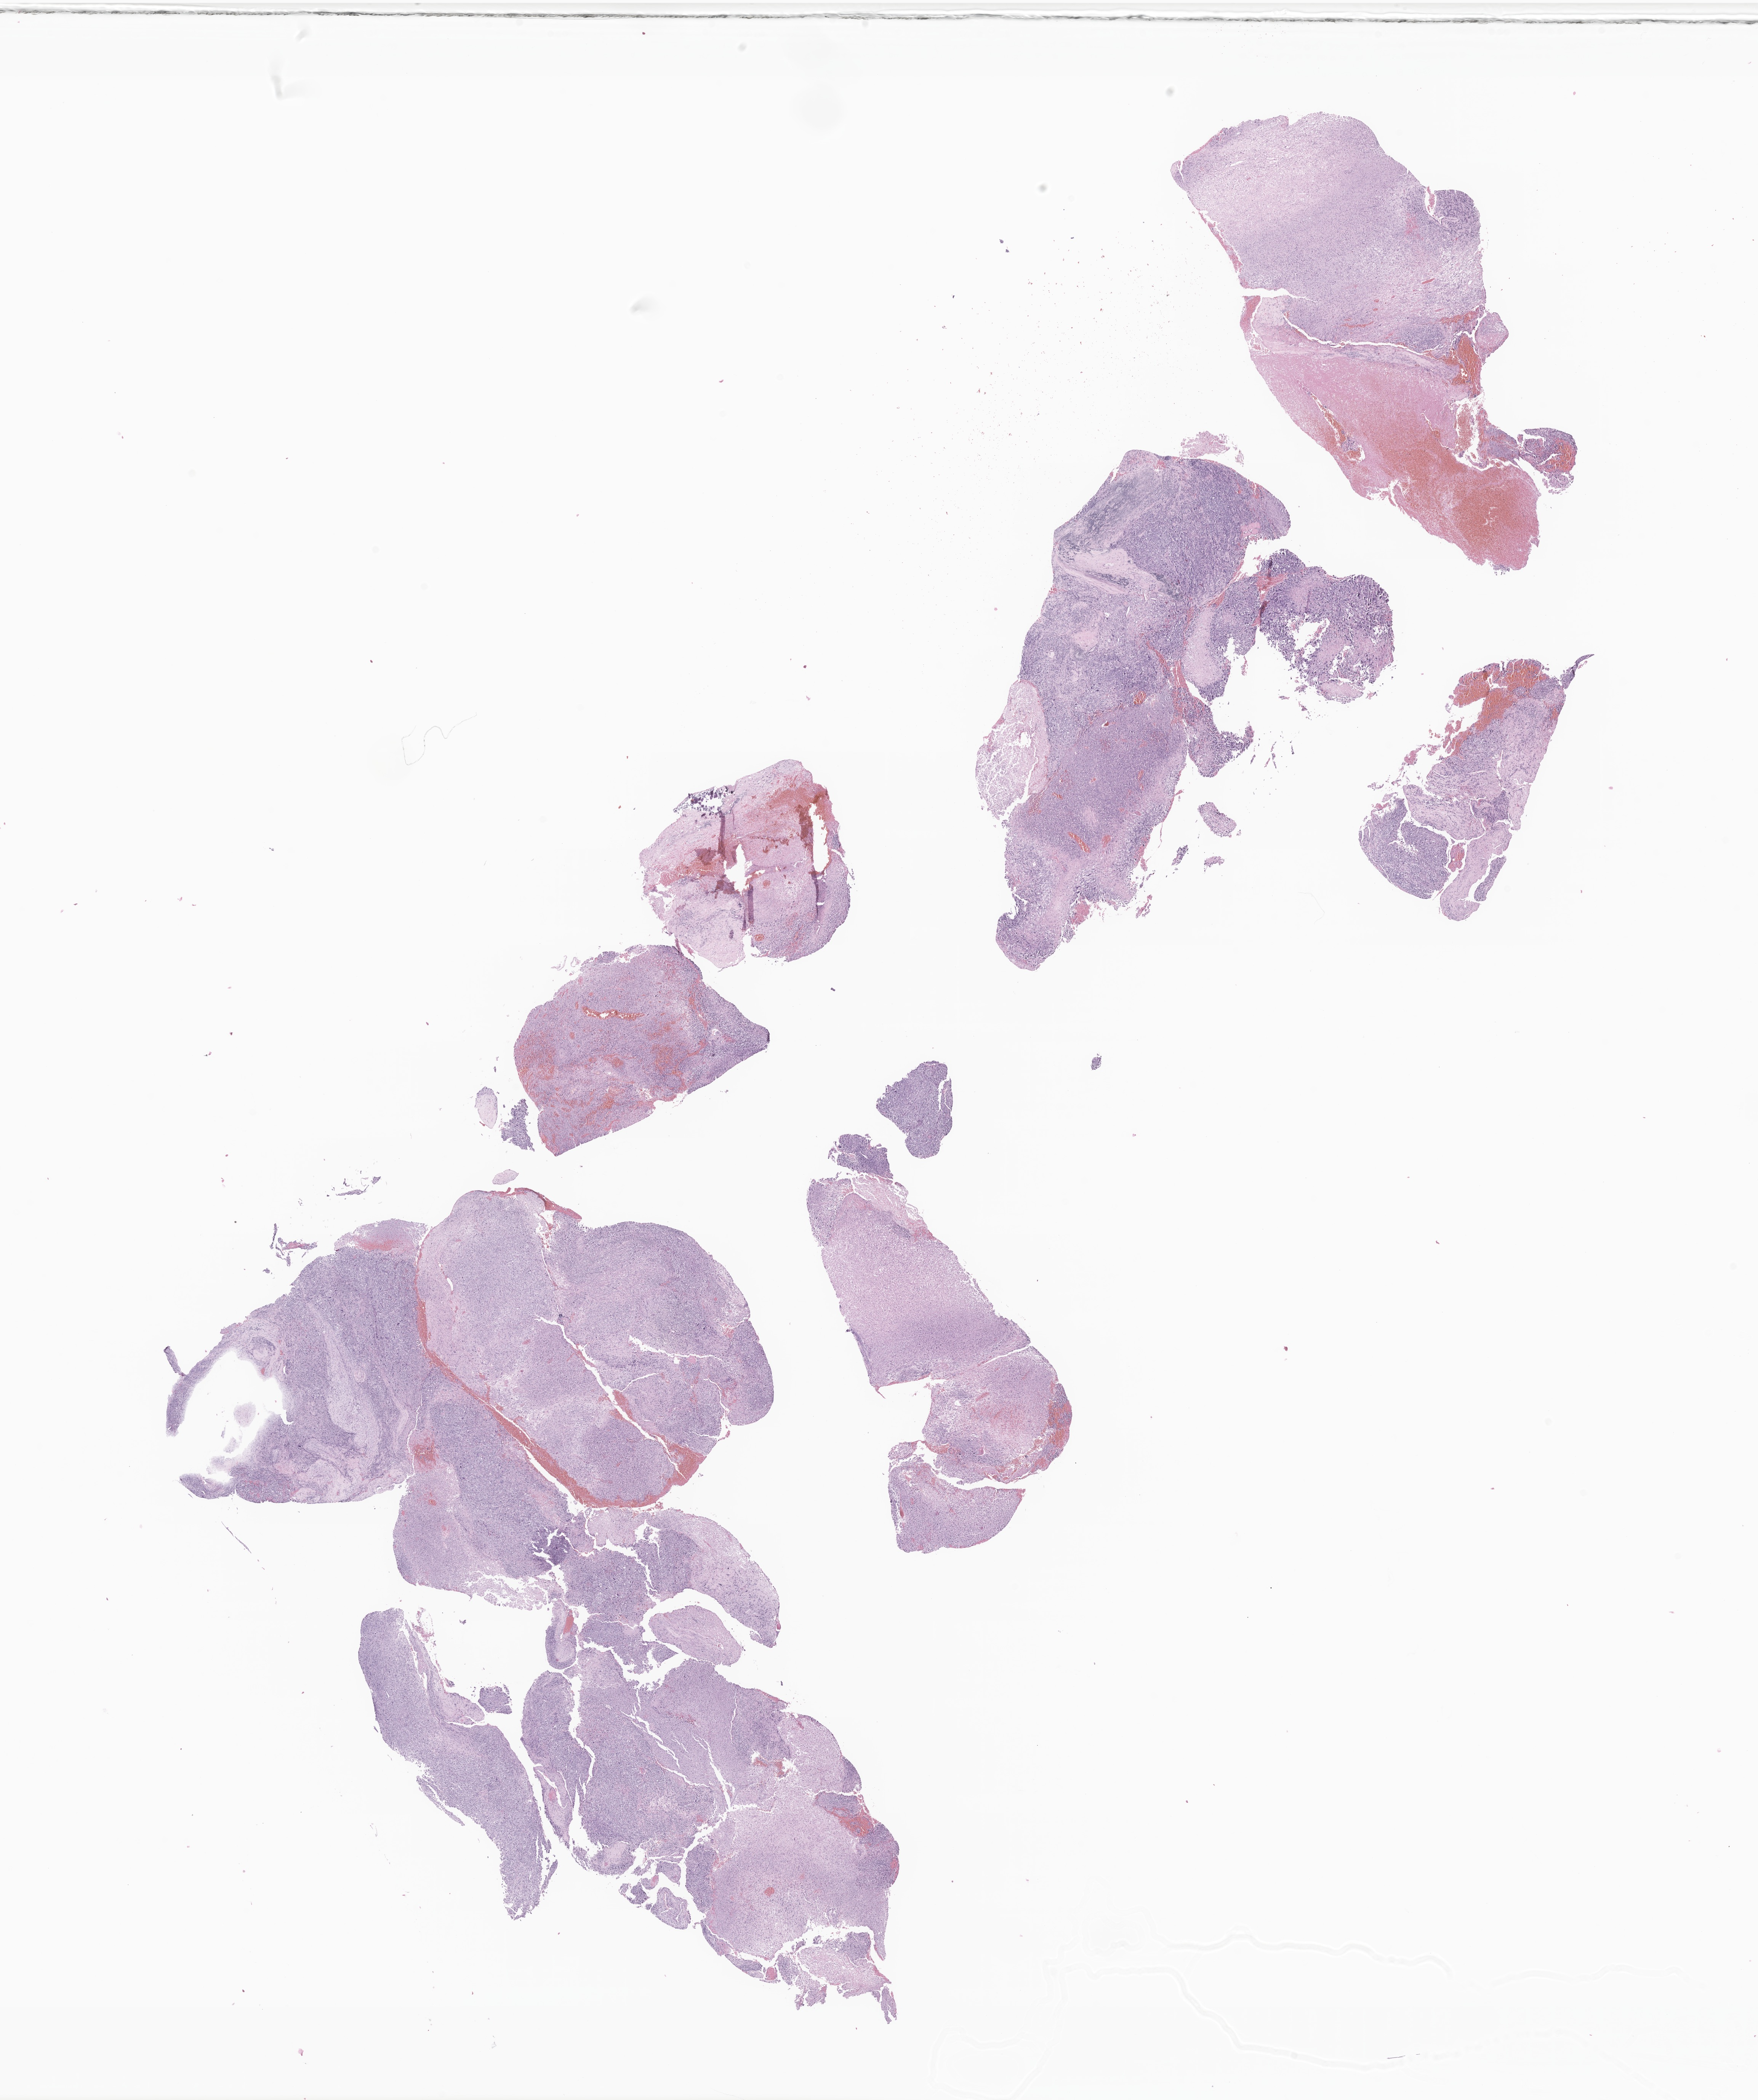
Whole-slide image, H&E stain of tumor tissue from the long bone of lower limb — whole scanned area (about 19.4 x 23.2 mm) shown as a low-resolution overview. FFPE section. Patient: male, age 165 months (13 years 9 months).
* recorded diagnosis: Sarcoma, NOS